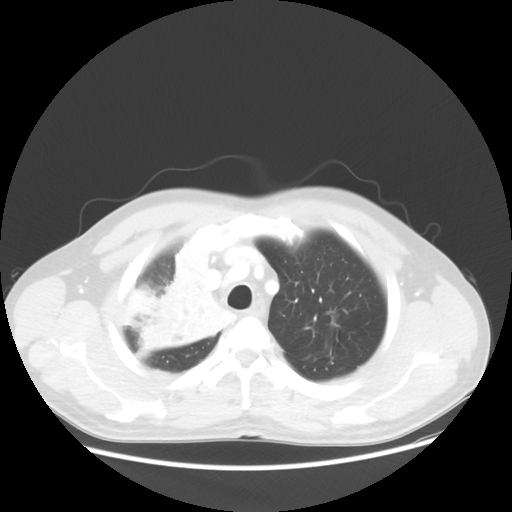
Chest CT, one axial slice. Slice 44 of 56 in the series (ordered by position). Reconstruction kernel STANDARD. Lung window (W 1500 / L -600 HU). 5 mm slice thickness. 512 × 512 image matrix, field of view 398 × 398 mm. Patient: male, 60 years. From the clinical record (not read from this slice): clinical TNM (as recorded): T2a N1 M0.
Outlined on this slice (rectangle marked by the reading radiologist):
- lung tumour (recorded histology: squamous cell carcinoma): bounding box [x1, y1, x2, y2] px = [132, 245, 237, 361]